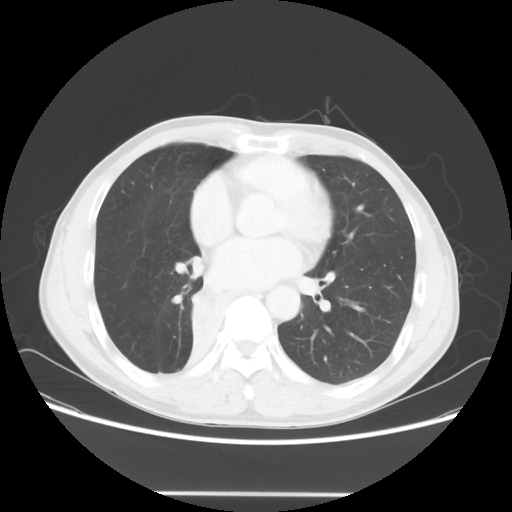
Chest CT, one axial slice. Position 28 of 62 along the scan axis. Reconstruction kernel STANDARD. 120 kVp. Lung window (W 1500 / L -600 HU). 5 mm slice thickness. 512 × 512 image matrix, field of view 393 × 393 mm. Patient: male, 47 years. Case-level facts recorded for this patient, not image findings: clinical TNM (as recorded): T2 N0 M0; histopathological grade: G2.
Outlined on this slice (rectangle marked by the reading radiologist):
- lung tumour (recorded histology: squamous cell carcinoma): bounding box [x1, y1, x2, y2] px = [188, 283, 240, 340]